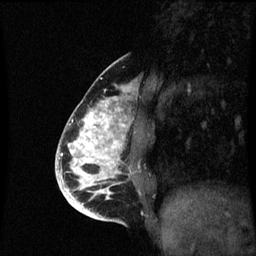
Breast MRI (dynamic contrast-enhanced), one sagittal slice. Position 23 of 60 along the scan axis. Dynamic contrast-enhanced series, image 2 of 3 at this slice position (ordered by acquisition). 1.5 T. TE 4.2 ms, TR 8.9 ms. 2 mm slice thickness. 256 × 256 image matrix. Patient: female, 35 years. Case-level facts recorded for this patient, not image findings: setting: breast cancer imaged before/during neoadjuvant chemotherapy; receptor status: HR-positive, HER2-negative.
Annotated regions visible in this slice (semi-automatic segmentation, software-assisted and operator-edited):
- analysis volume of interest (the breast-tissue region the enhancement analysis was run in; not a lesion): bounding box (x1, y1, x2, y2) in pixels: (66, 98, 135, 215)
- tumour enhancement mask (voxels above the 70 % enhancement threshold inside the analysis volume of interest): (66, 100, 126, 215)